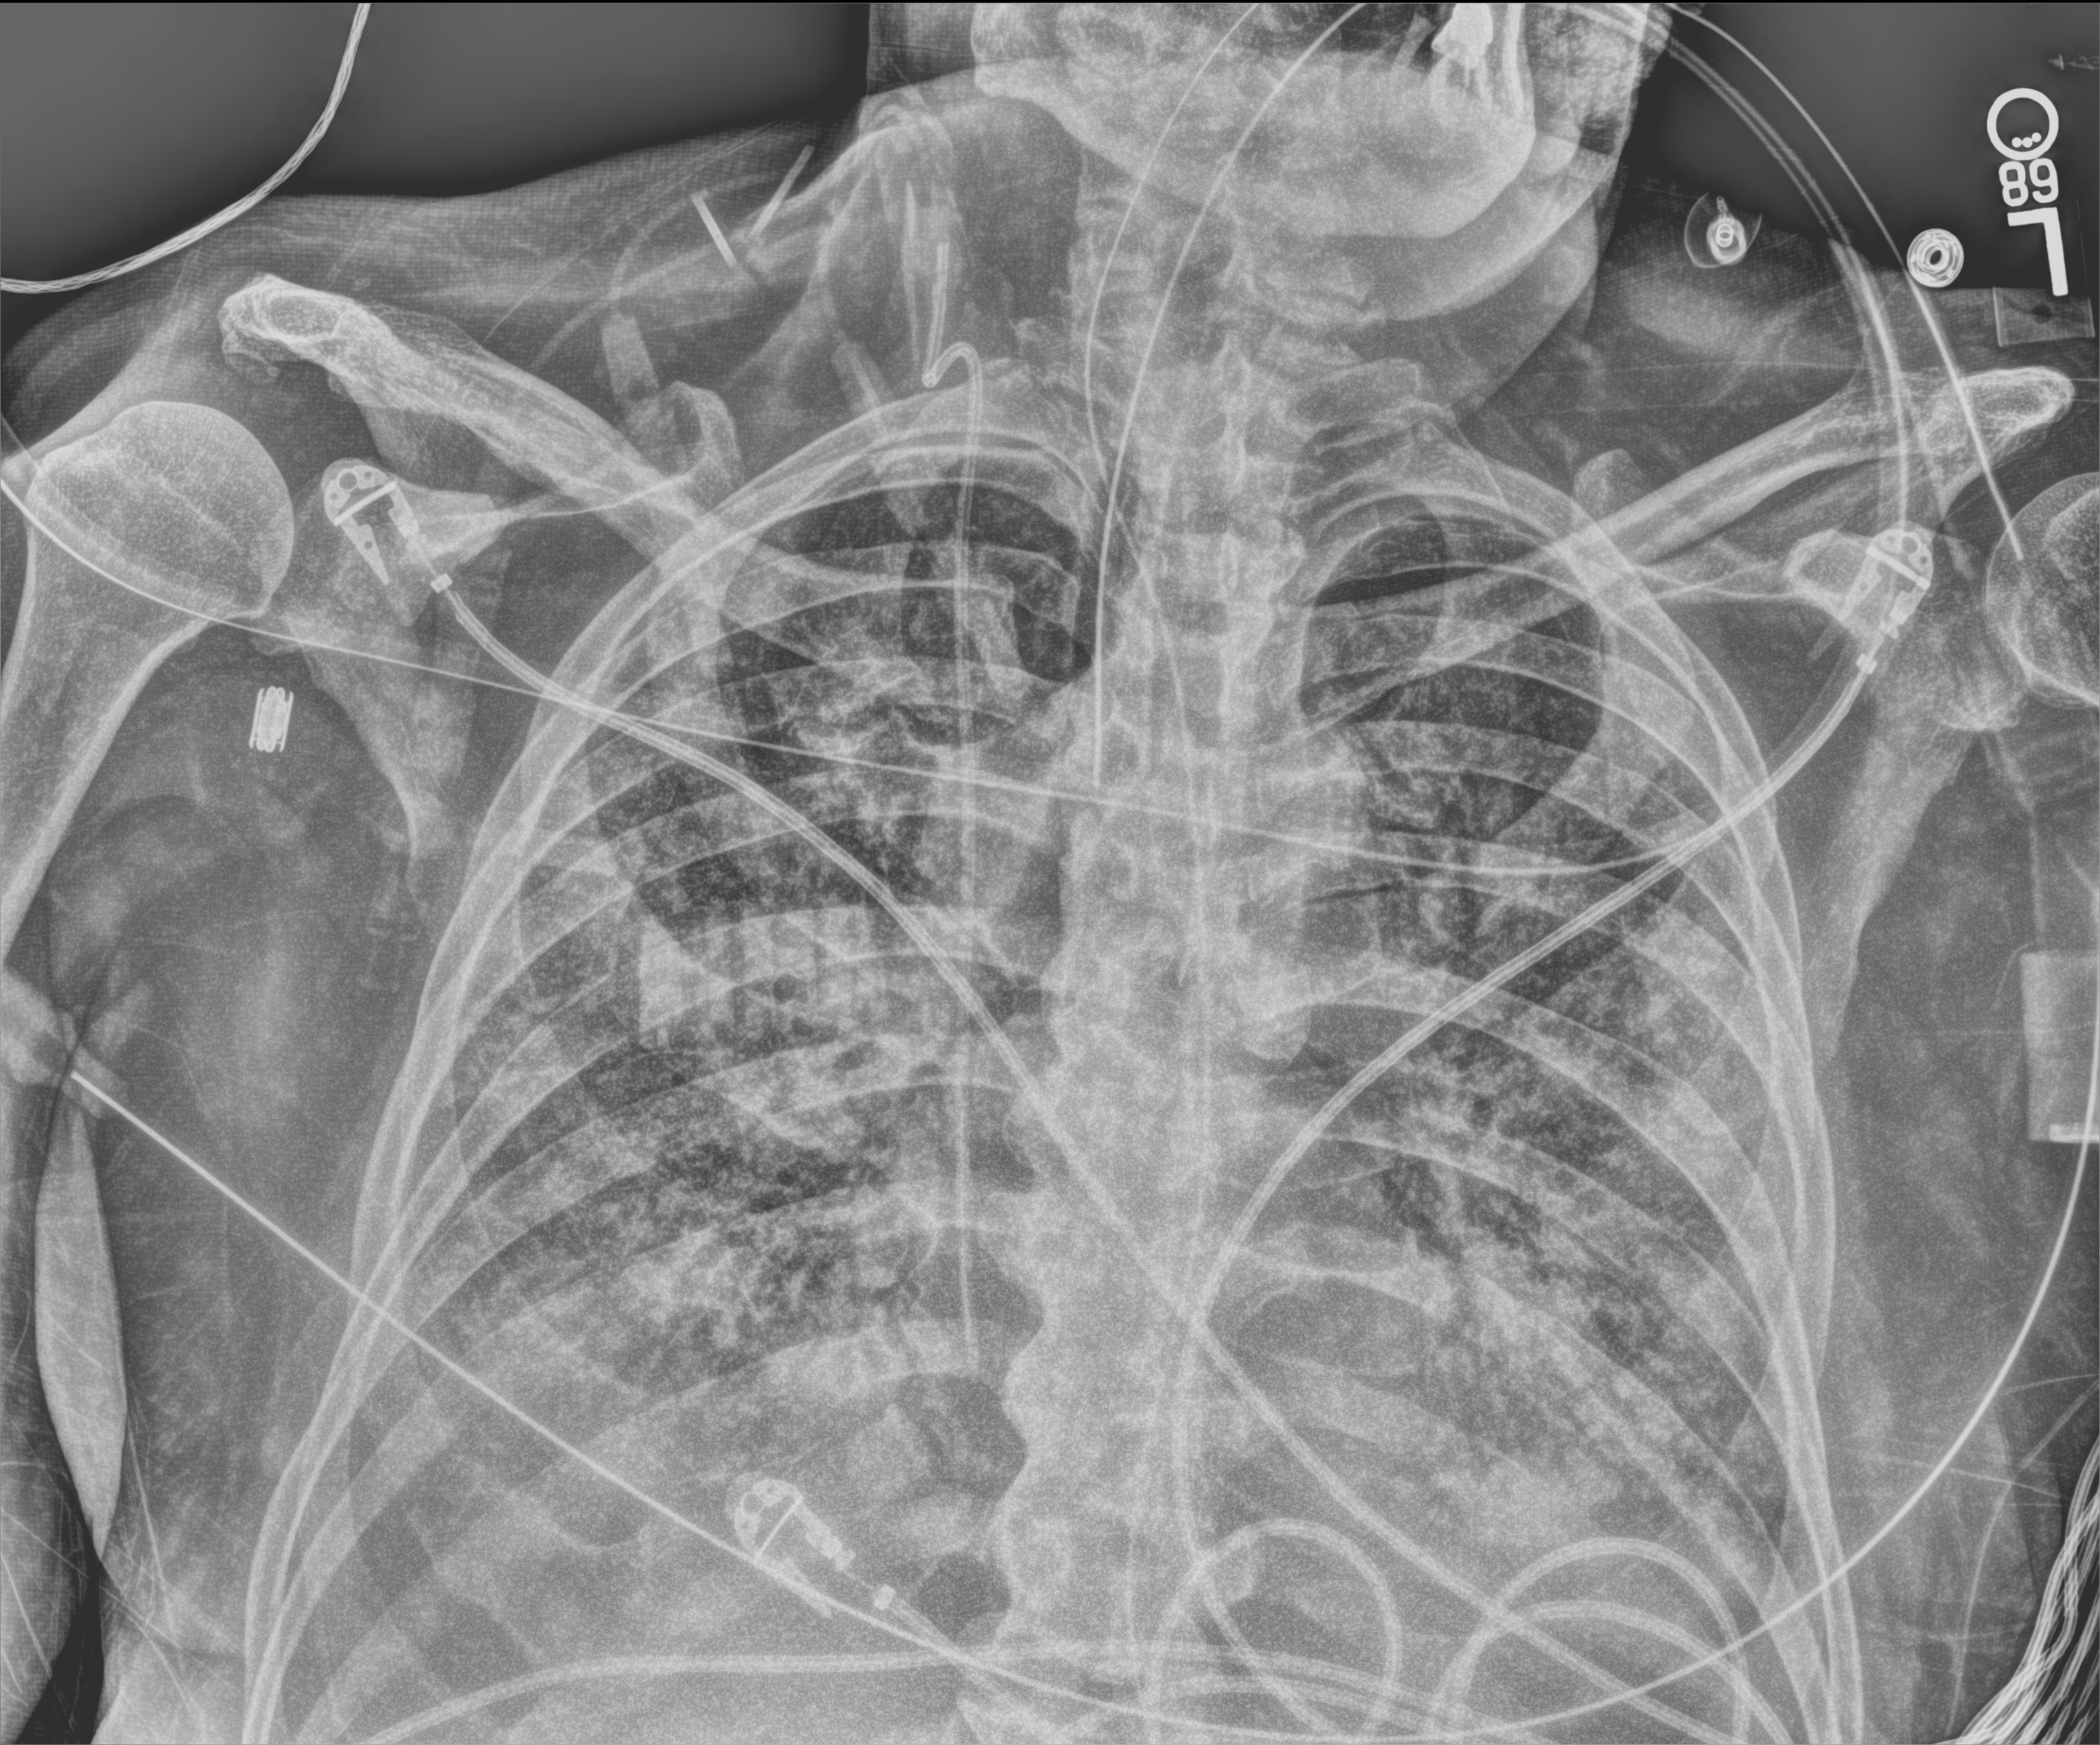
Chest X-ray (portable); anteroposterior (AP) projection. Male patient hospitalised with COVID-19, age 75–90 years.
Admission-level facts for this patient (not findings on this image; timing relative to this image not recorded): diabetes (admission record): no; admitted to intensive care during this hospital stay: yes.